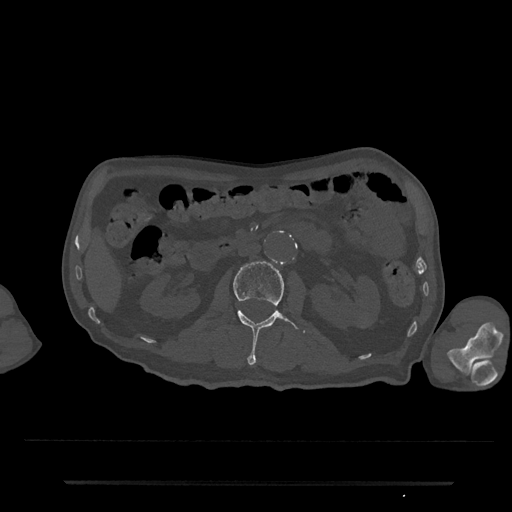
CT including the spine, one axial slice. Position 57 of 797 along the scan axis. Bone window (W 1800 / L 400 HU). 0.5 mm slice thickness. 512 × 512 image matrix, field of view 427 × 427 mm. Male patient, age 74 years. Case-level facts recorded for this patient, not image findings: primary cancer: prostate.
Annotated regions visible in this slice (semi-automatic segmentation, software-assisted and operator-edited):
- L2 vertebra: bounding box (x1, y1, x2, y2) in pixels: (233, 261, 306, 365)